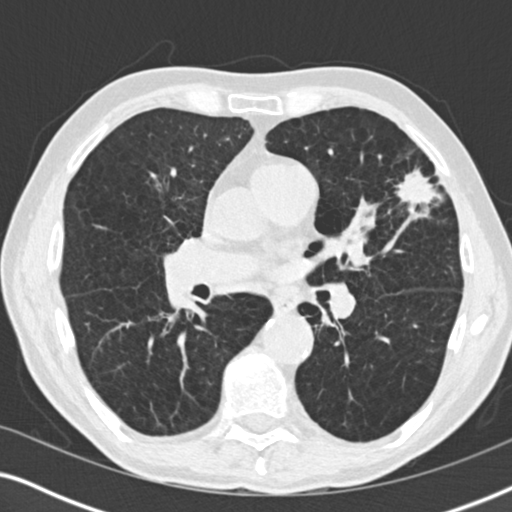
Low-dose screening chest CT, one axial slice; slice 102 of 196 in the series (ordered by position); 120 kVp; lung window (W 1500 / L -600 HU); 2 mm slice thickness; 512 × 512 image matrix.
Annotated regions visible in this slice (expert manual segmentation):
- lesion 1 (tumor, upper lobe of left lung): bounding box <397,170,438,208> (left, top, right, bottom; pixels)